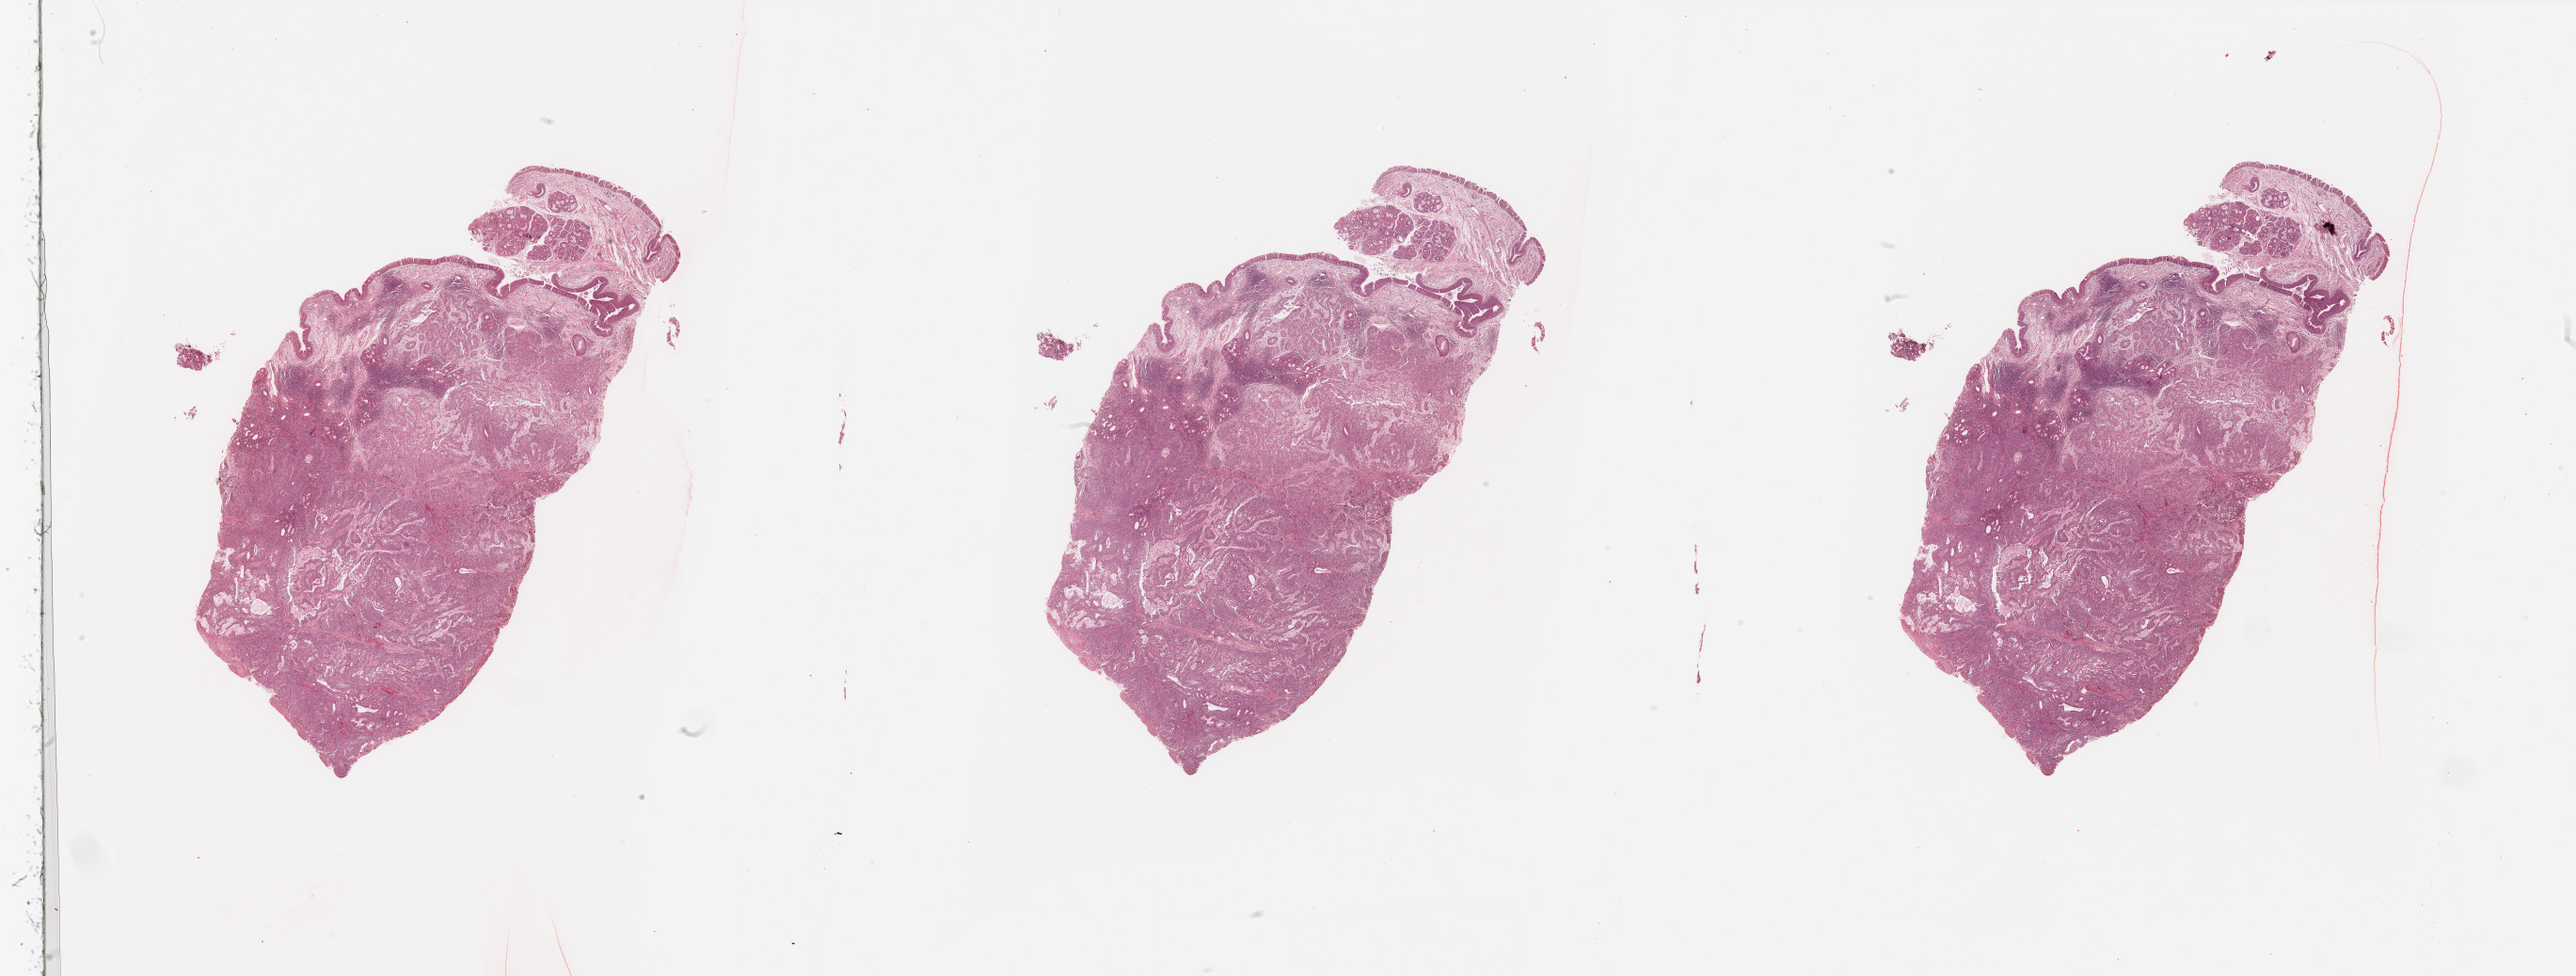
Hematoxylin and eosin (H&E) stained whole-slide image, a low-resolution overview of the entire scanned area, about 43.3 x 16.4 mm (from a 20x scan), head and neck, tissue type not recorded. Patient: male, age 60 years.
Patient diagnosis: Squamous cell carcinoma, NOS (larynx, NOS).